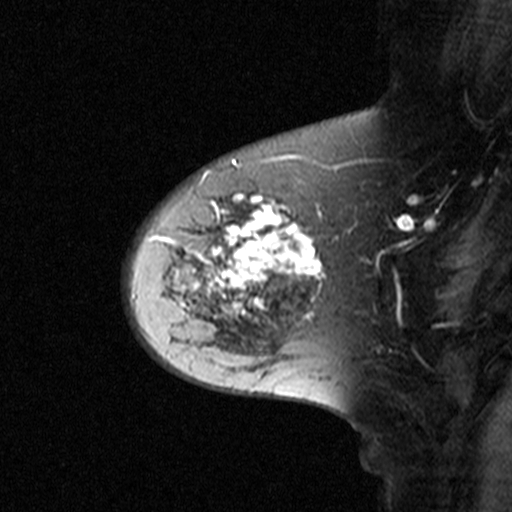
Breast MRI (dynamic contrast-enhanced), one sagittal slice. Slice 31 of 44 in the series (ordered by position). Dynamic contrast-enhanced study with each time point stored as its own series, time point 2 of 3 at this slice position (early post-contrast, ordered by acquisition time). 1.5 T. TE 4.5 ms, TR 11 ms. 3 mm slice thickness. 512 × 512 image matrix. Patient: female, 65 years. Case-level facts recorded for this patient, not image findings: setting: breast cancer imaged before/during neoadjuvant chemotherapy; receptor status: HER2-positive.
Structures marked on this image (semi-automatic segmentation, software-assisted and operator-edited):
- analysis volume of interest (the breast-tissue region the enhancement analysis was run in; not a lesion): bounding box (x1, y1, x2, y2) in pixels: (160, 172, 329, 345)
- tumour enhancement mask (voxels above the 90 % enhancement threshold inside the analysis volume of interest): (183, 194, 326, 318)